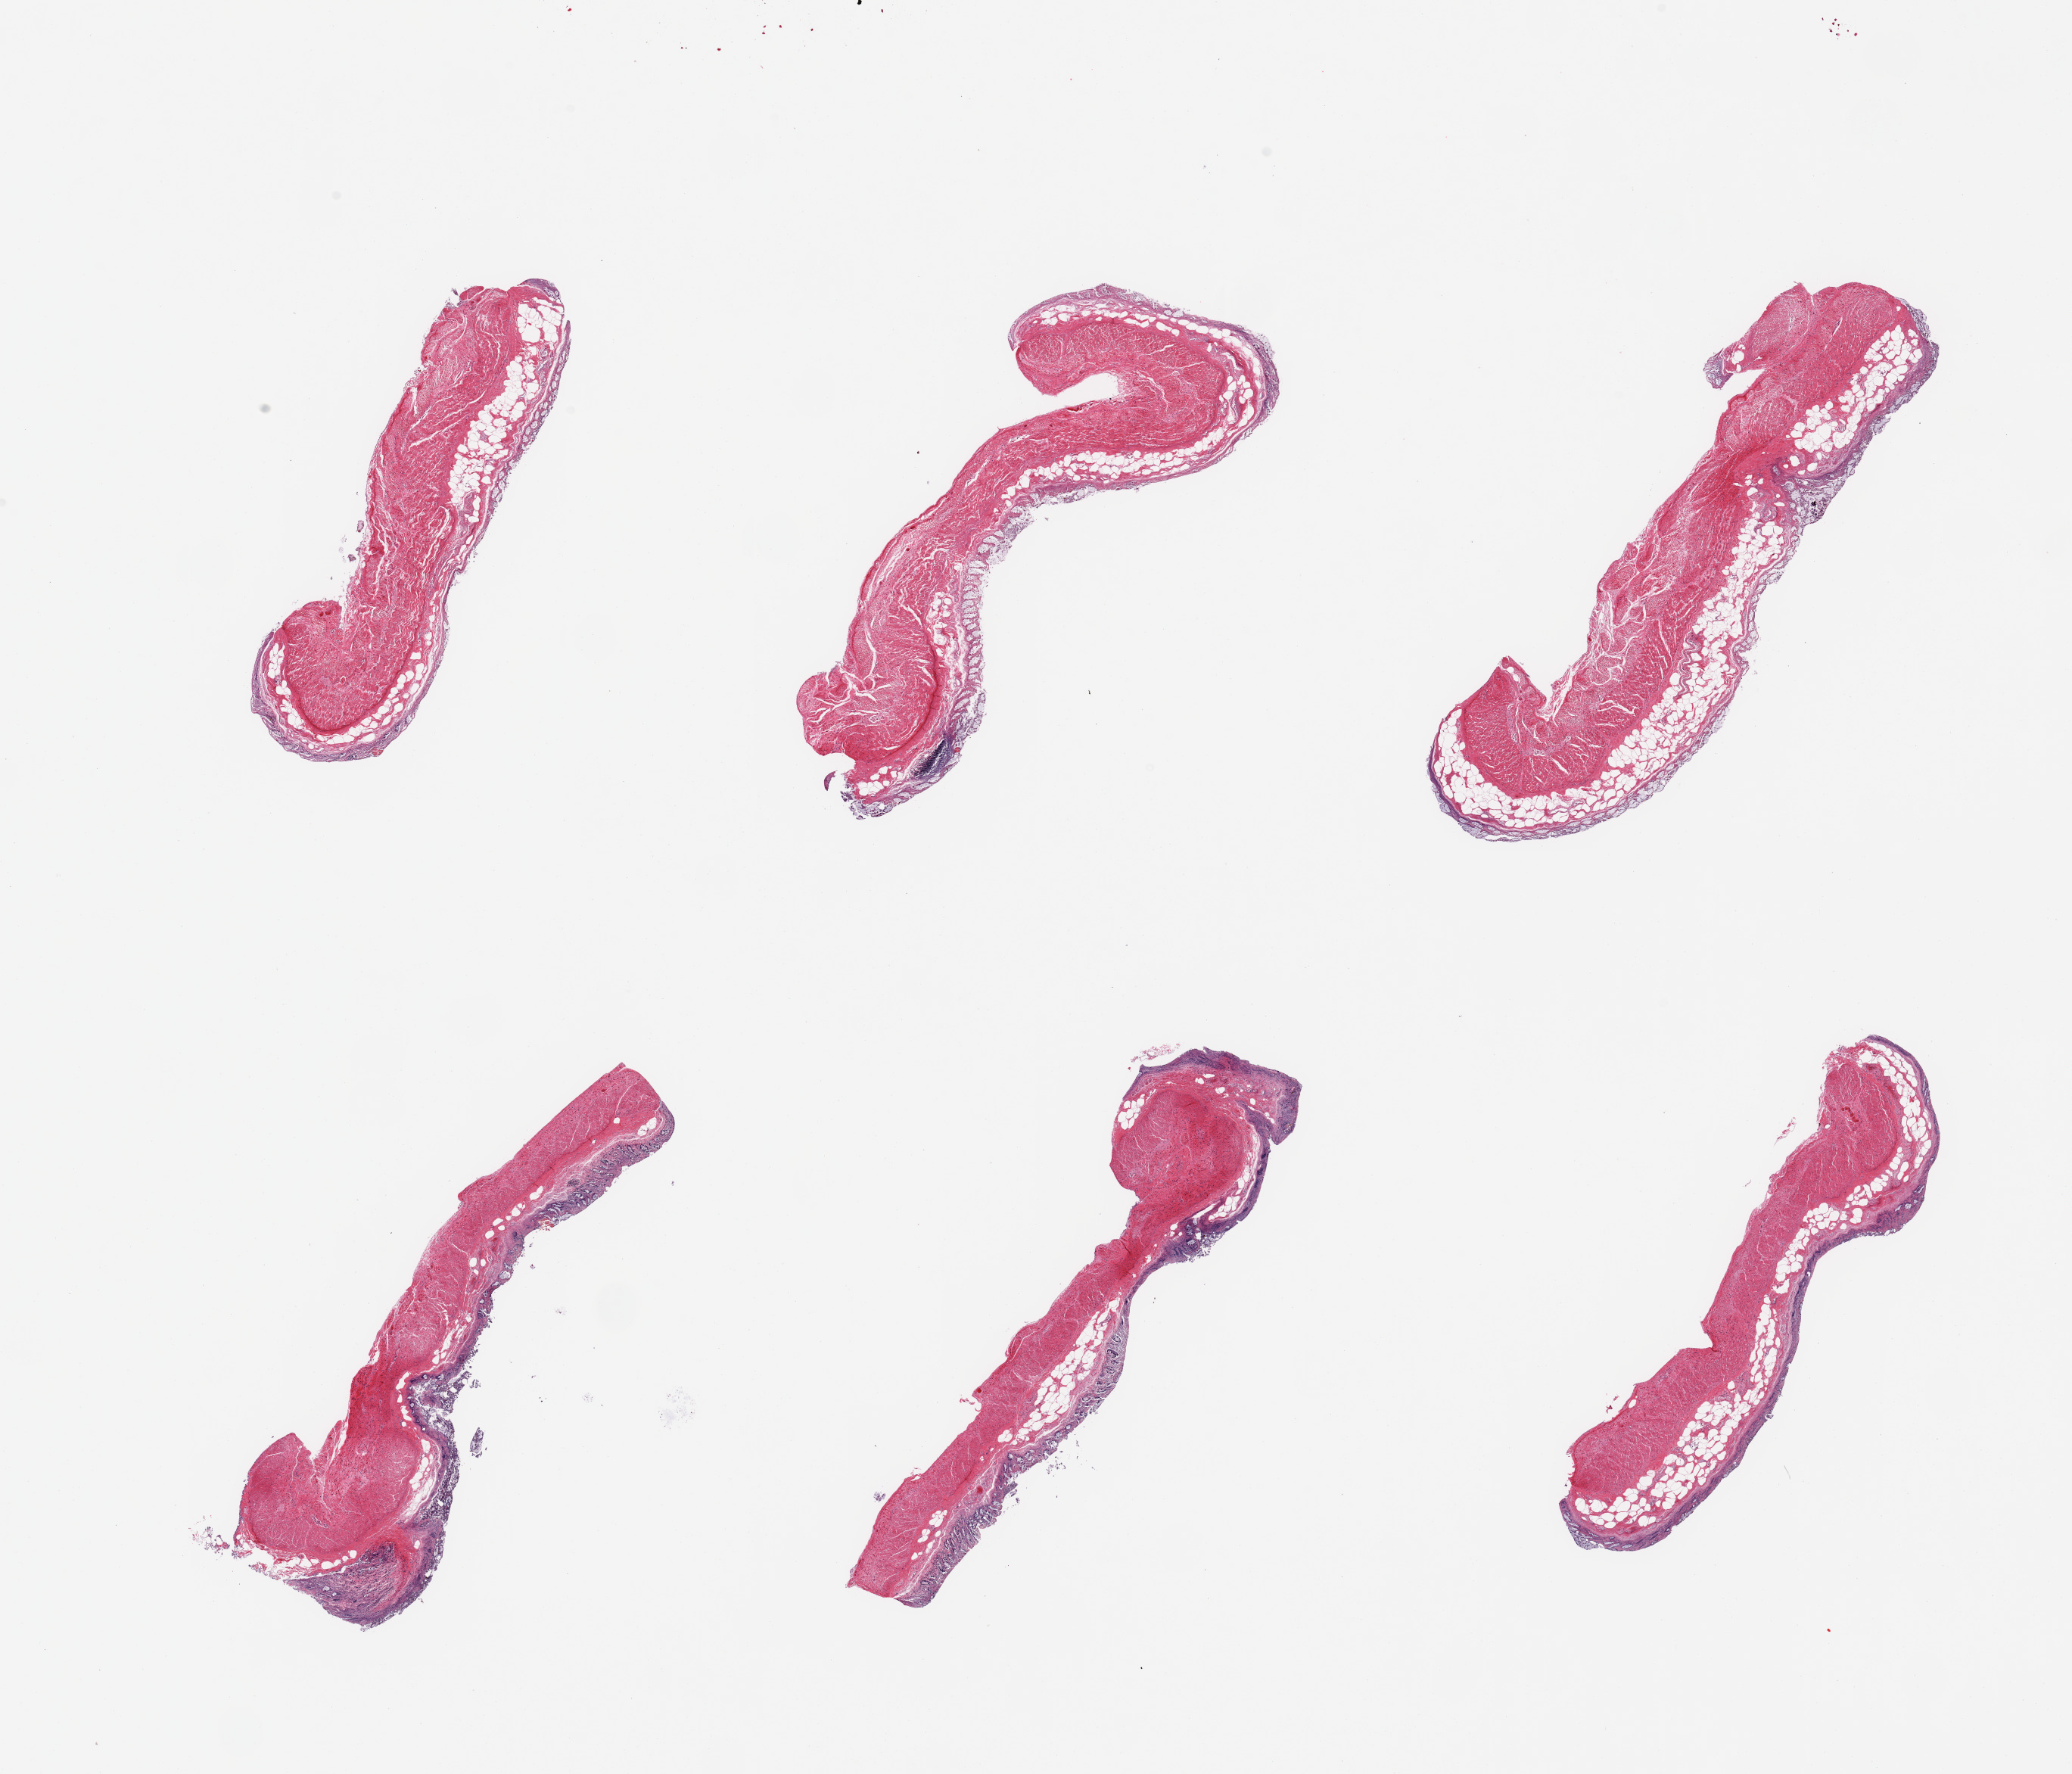
Digitized hematoxylin and eosin (H&E)-stained section — a low-resolution overview of the entire scanned area, about 21.7 x 18.5 mm, PAXgene-fixed paraffin-embedded (PFPE) section, section of transverse colon (target tissue), donor tissue sample. Male donor.
Pathologist's review note for this sample: 6 pieces glandular mucosa totally autolyzed, partallly sloughed, ~0.1mm.